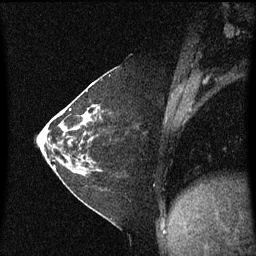
Breast MRI (dynamic contrast-enhanced), one sagittal slice. Position 24 of 60 along the scan axis. Dynamic contrast-enhanced series, image 2 of 3 at this slice position (ordered by acquisition). 1.5 T. TE 4.2 ms, TR 8.4 ms. 2 mm slice thickness. 256 × 256 image matrix. Patient: female, 36 years. Case-level facts recorded for this patient, not image findings: setting: breast cancer imaged before/during neoadjuvant chemotherapy; receptor status: HR-positive, HER2-negative.
Structures marked on this image (semi-automatically segmented with operator editing):
- analysis volume of interest (the breast-tissue region the enhancement analysis was run in; not a lesion): box from (x=66, y=102) to (x=113, y=177) px
- tumour enhancement mask (voxels above the 70 % enhancement threshold inside the analysis volume of interest): (x=66, y=112)–(x=92, y=129)